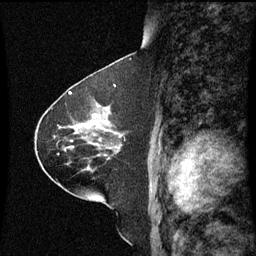
Breast MRI (dynamic contrast-enhanced), one sagittal slice; position 37 of 60 along the scan axis; dynamic contrast-enhanced series, image 2 of 3 at this slice position (ordered by acquisition); 1.5 T; TE 4.2 ms, TR 8.9 ms; 256 × 256 image matrix, field of view 200 × 200 mm. Patient: female, 63 years. From the clinical record (not read from this slice): setting: breast cancer imaged before/during neoadjuvant chemotherapy; receptor status: HR-positive, HER2-negative.
Annotated regions visible in this slice (semi-automatic segmentation, software-assisted and operator-edited):
- analysis volume of interest (the breast-tissue region the enhancement analysis was run in; not a lesion): bounding box [x1, y1, x2, y2] px = [77, 100, 123, 151]
- tumour enhancement mask (voxels above the 70 % enhancement threshold inside the analysis volume of interest): [93, 114, 97, 119]